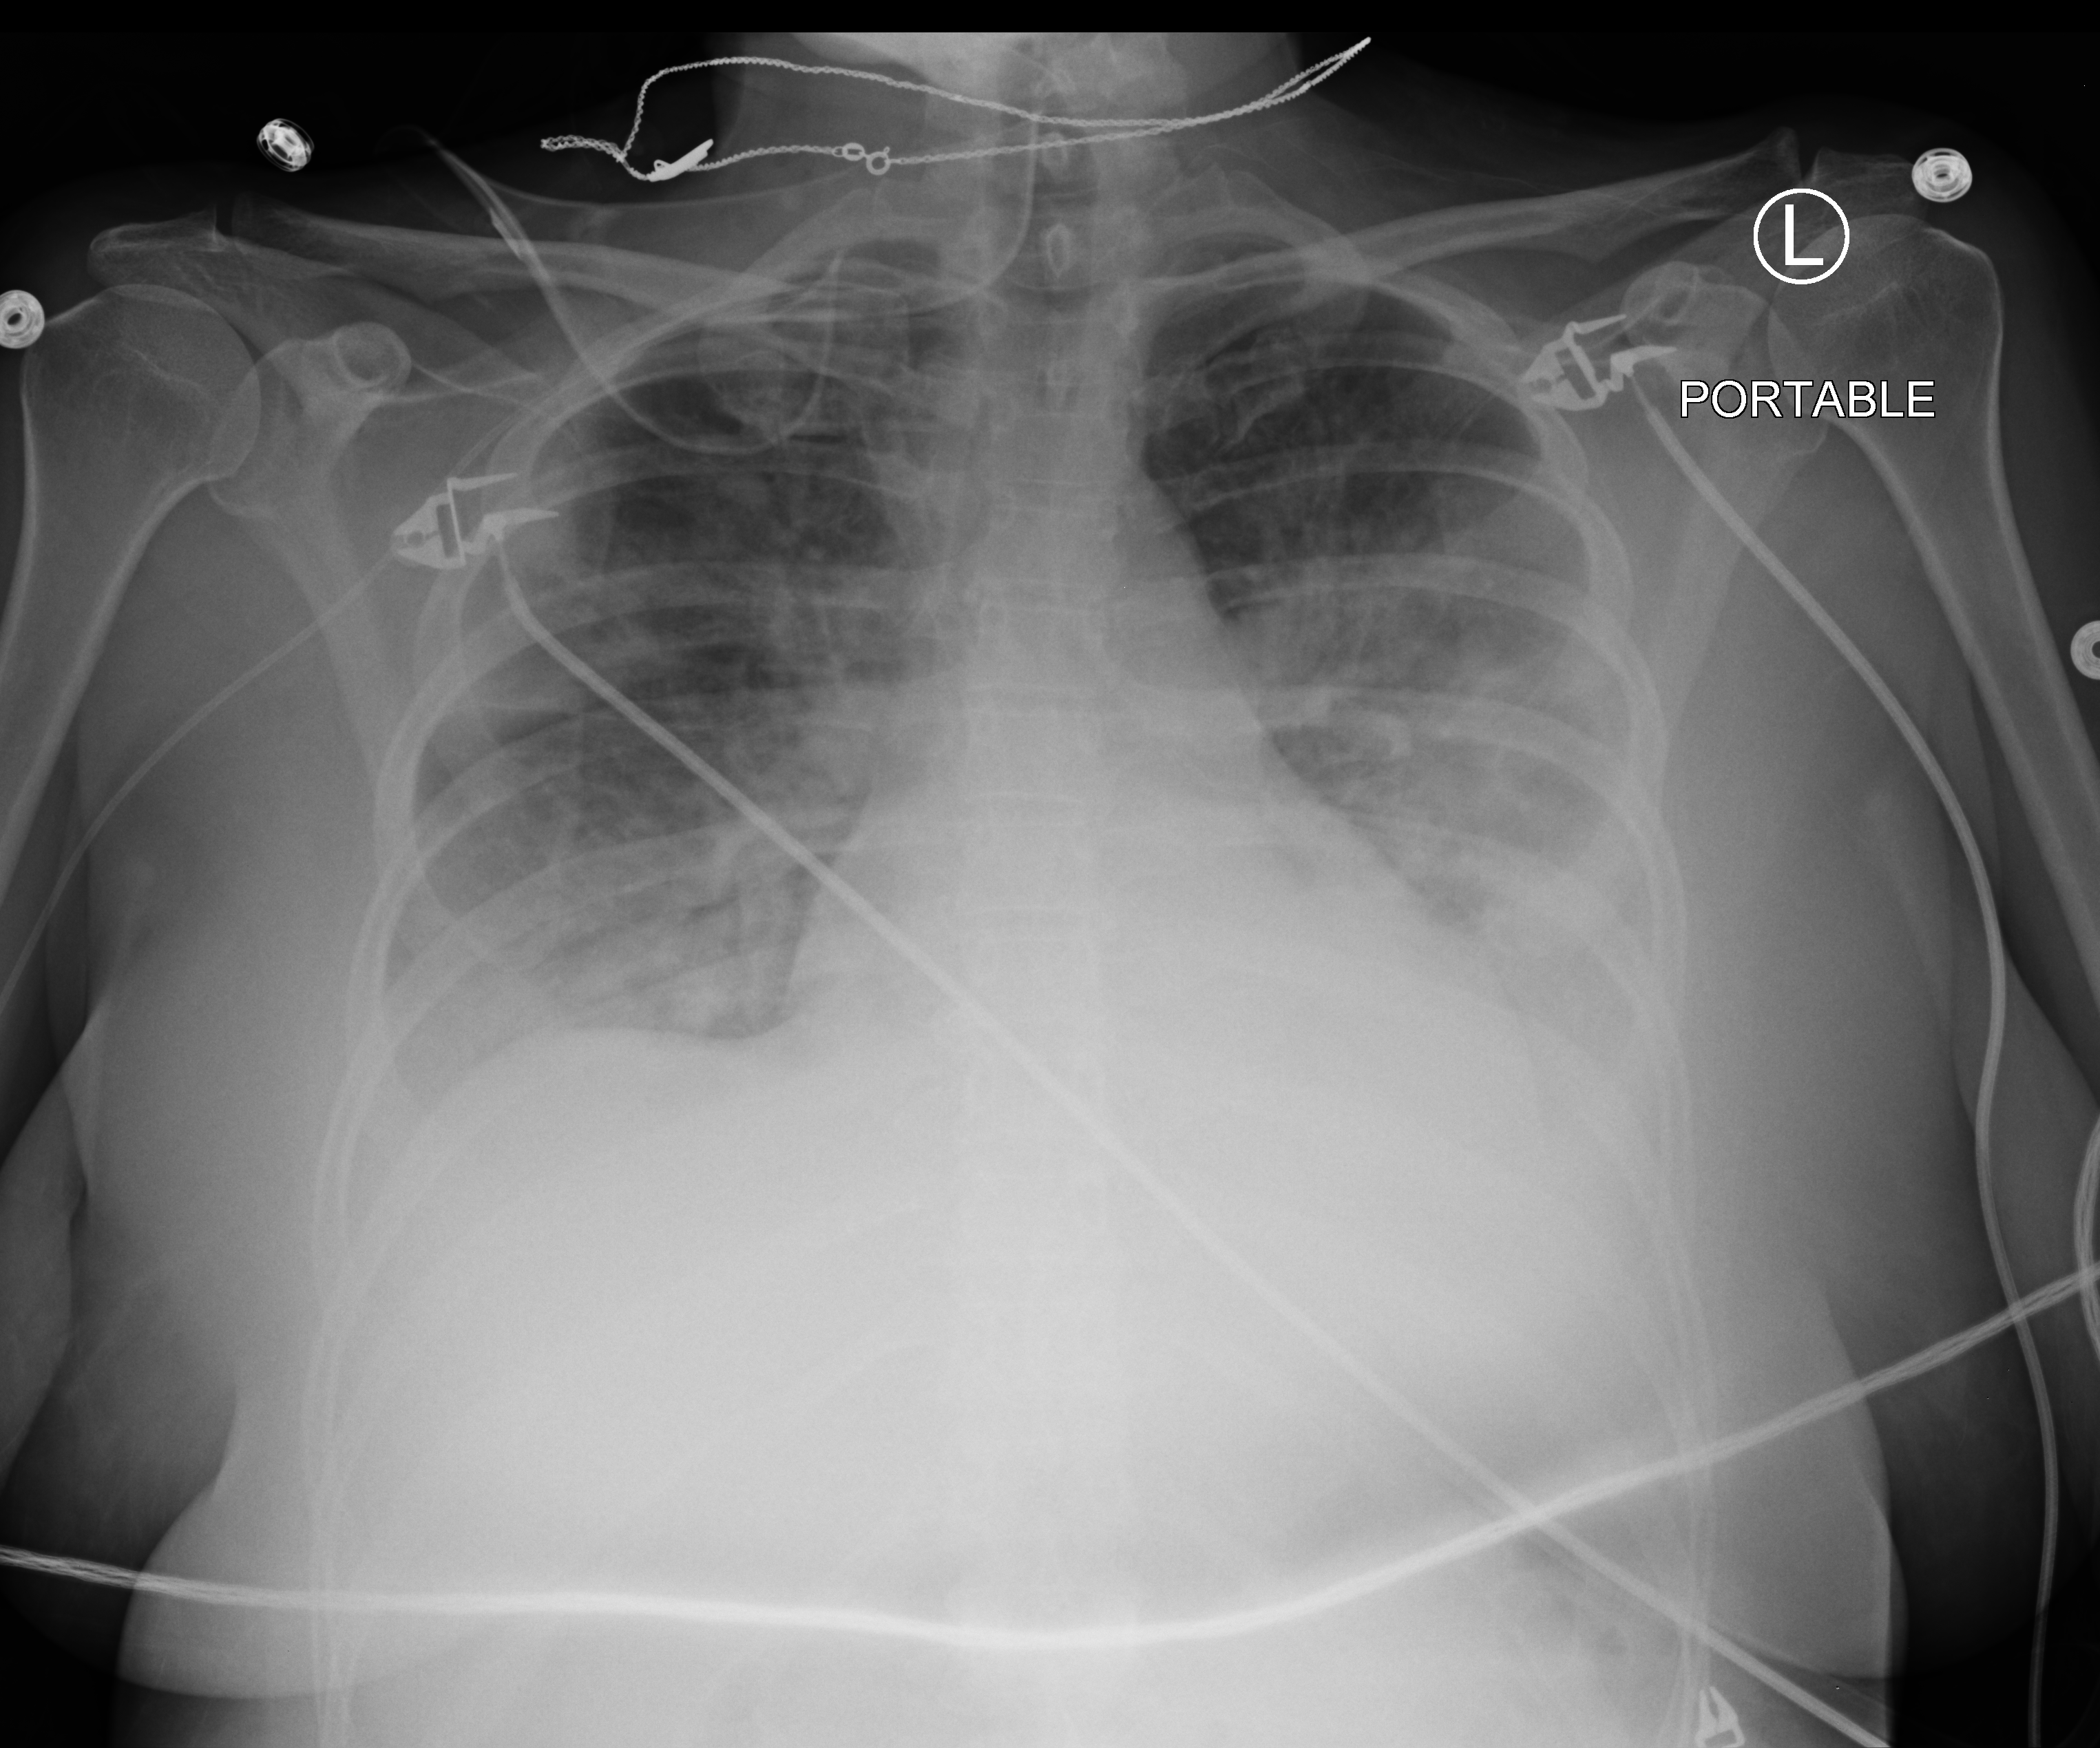
Portable chest radiograph, anteroposterior (AP) projection. Female patient hospitalised with COVID-19, age 18–59 years.
Hospital-stay facts (about this admission, not read from this image; timing relative to this image not recorded): diabetes (admission record): yes; hypertension (admission record): no; admitted to intensive care during this hospital stay: no.